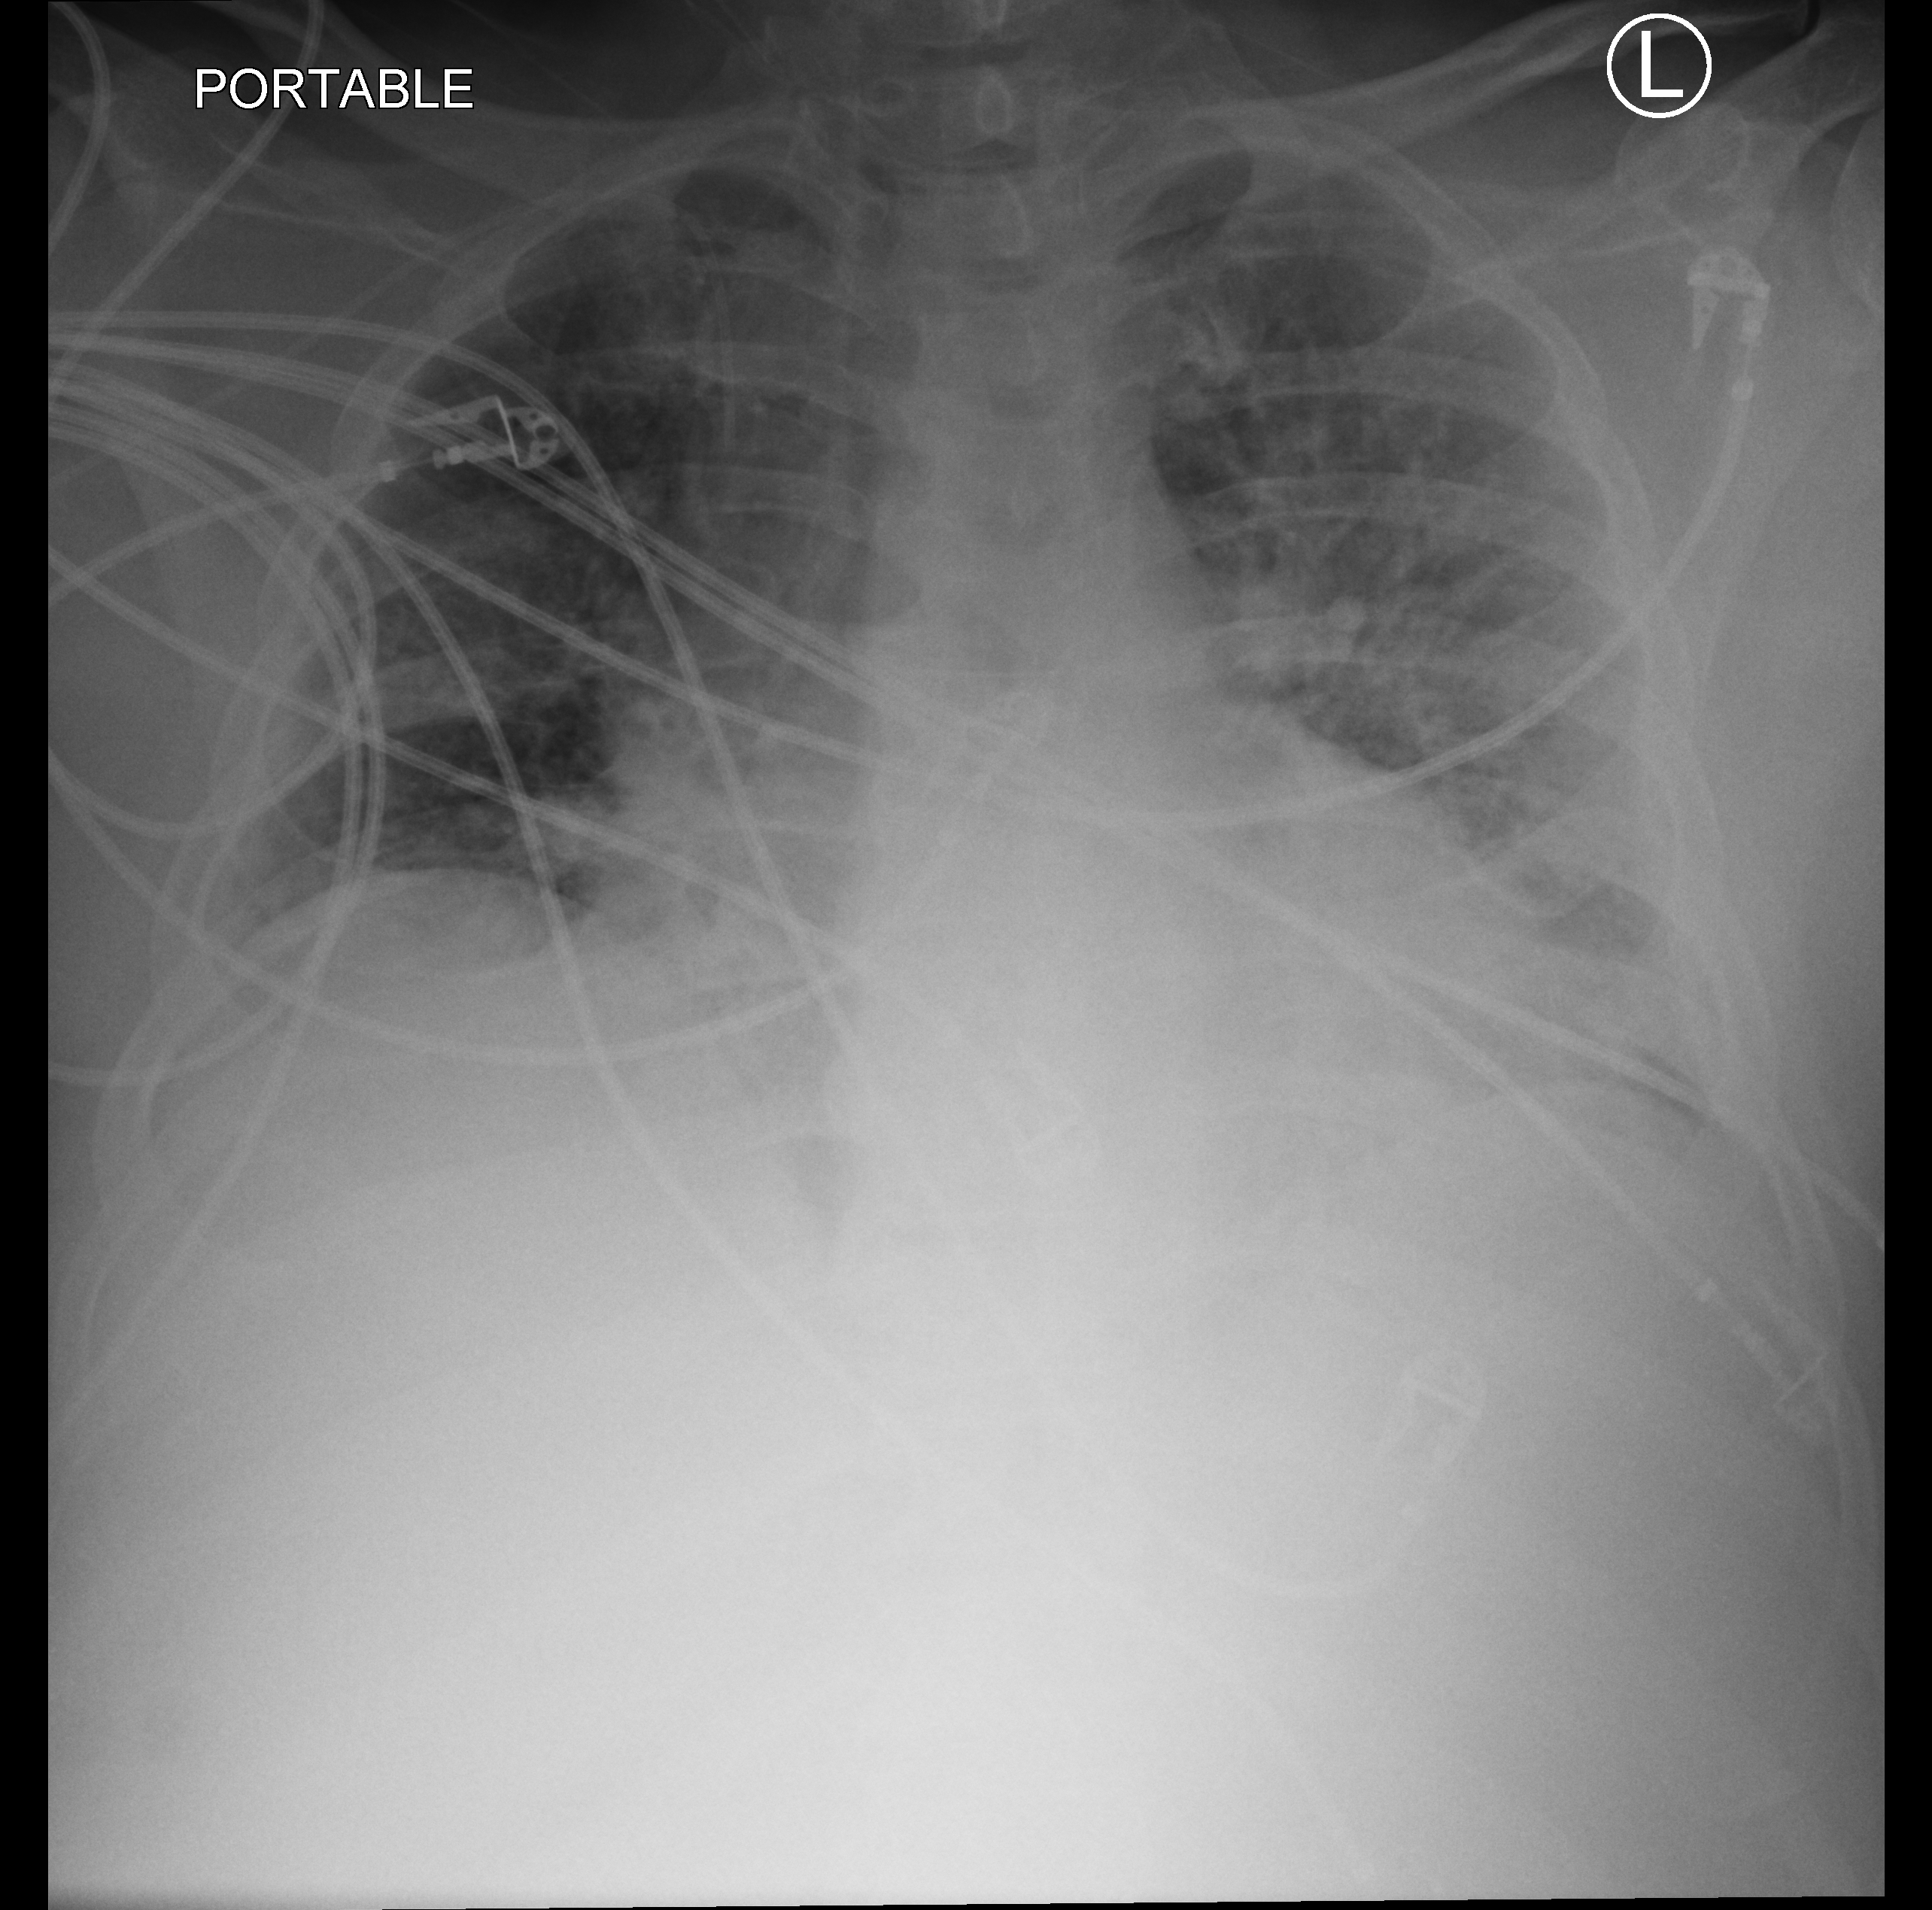
Chest X-ray (portable), anteroposterior (AP) projection. Patient hospitalised with COVID-19; male, aged 18–59 years.
Admission-level facts for this patient (not findings on this image; timing relative to this image not recorded): hypertension (admission record): yes; diabetes (admission record): no.